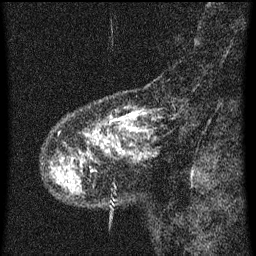
Breast MRI (dynamic contrast-enhanced), one sagittal slice; position 10 of 60 along the scan axis; dynamic contrast-enhanced series, image 2 of 3 at this slice position (ordered by acquisition); 1.5 T; TE 4.2 ms, TR 8 ms; 256 × 256 image matrix. Patient: female, 55 years.
Outlined on this slice (semi-automatically segmented with operator editing):
- analysis volume of interest (the breast-tissue region the enhancement analysis was run in; not a lesion): box from (x=52, y=96) to (x=161, y=159) px
- tumour enhancement mask (voxels above the 70 % enhancement threshold inside the analysis volume of interest): (x=120, y=112)–(x=139, y=121)